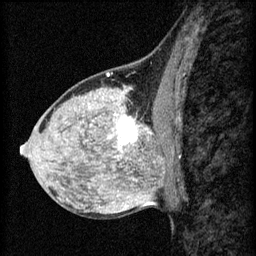
Breast MRI (dynamic contrast-enhanced), one sagittal slice; position 29 of 60 along the scan axis; 3 images stored at this slice position (order not interpretable as contrast timing); 1.5 T; TE 4.2 ms, TR 8.2 ms; 2 mm slice thickness; 256 × 256 image matrix, field of view 180 × 180 mm. Female patient, age 40 years.
Outlined on this slice (semi-automatically segmented with operator editing):
- analysis volume of interest (the breast-tissue region the enhancement analysis was run in; not a lesion): bounding box <108,108,167,159> (left, top, right, bottom; pixels)
- tumour enhancement mask (voxels above the 70 % enhancement threshold inside the analysis volume of interest): <118,116,151,145>